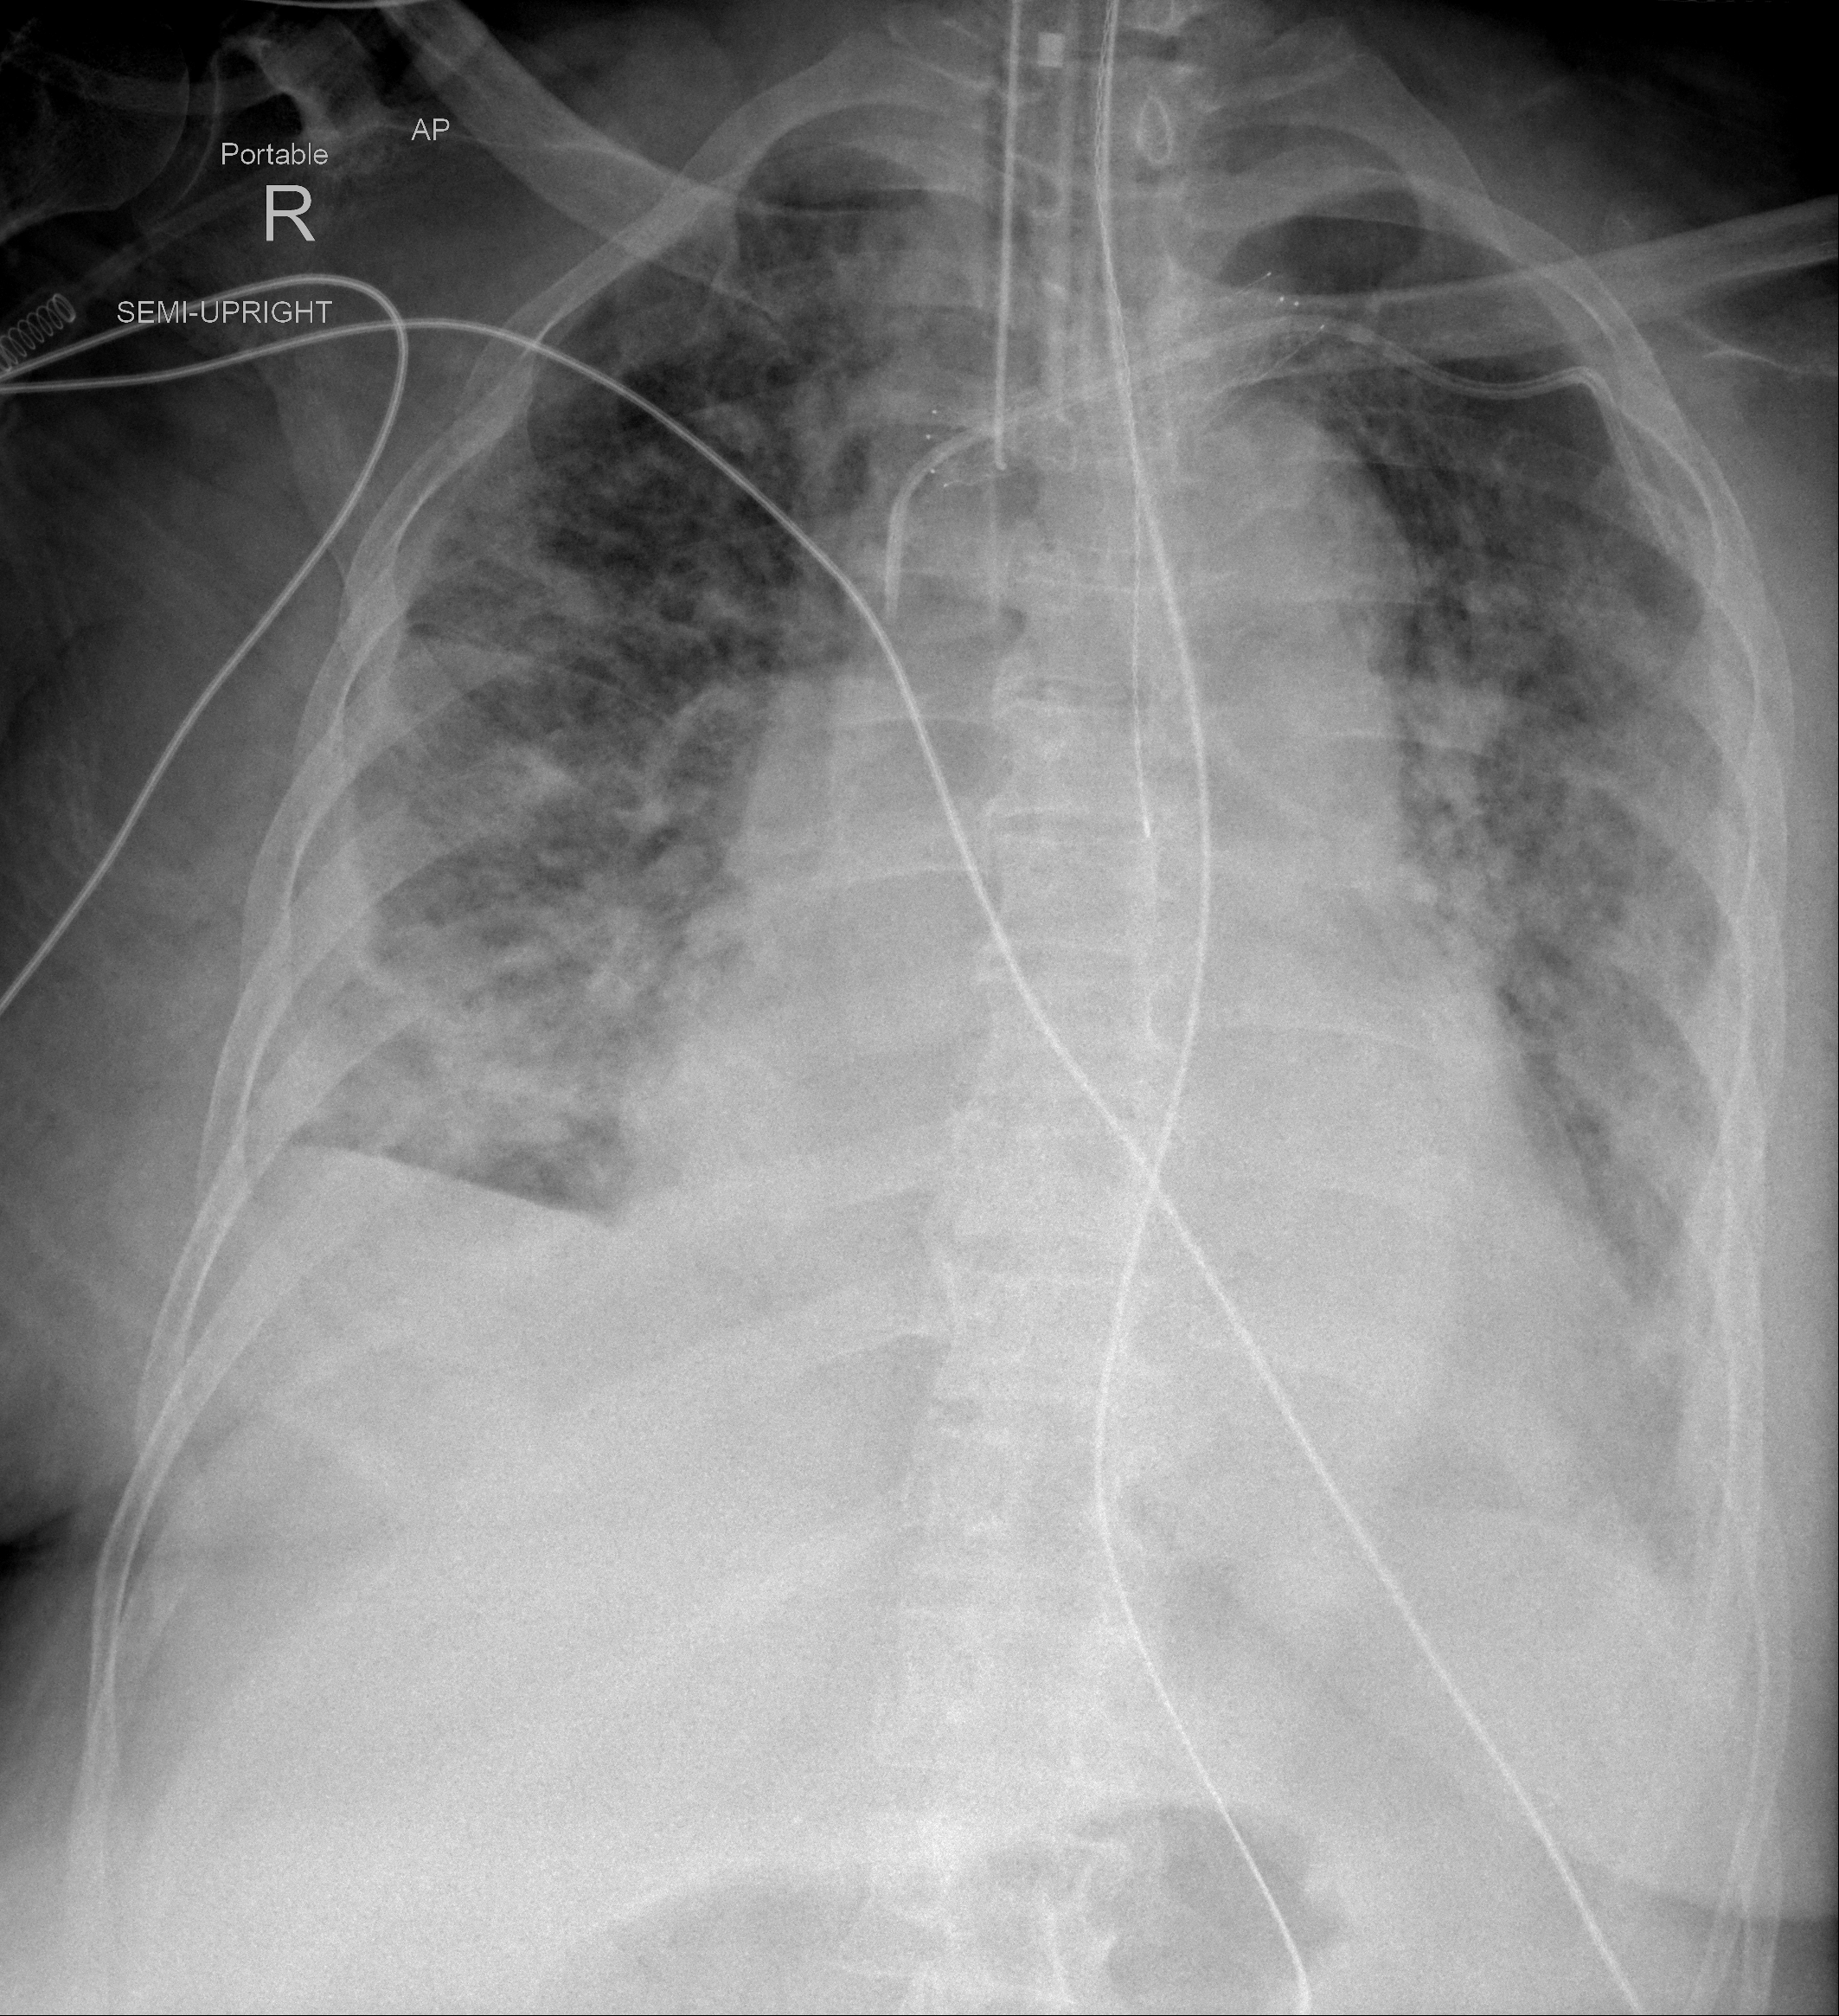
Chest X-ray (portable), AP projection. Female patient, age 64 years; imaged 5 days after the COVID-19 diagnosis.
Radiologist key findings (as recorded): diffuse patchy airspace disease in both lungs.